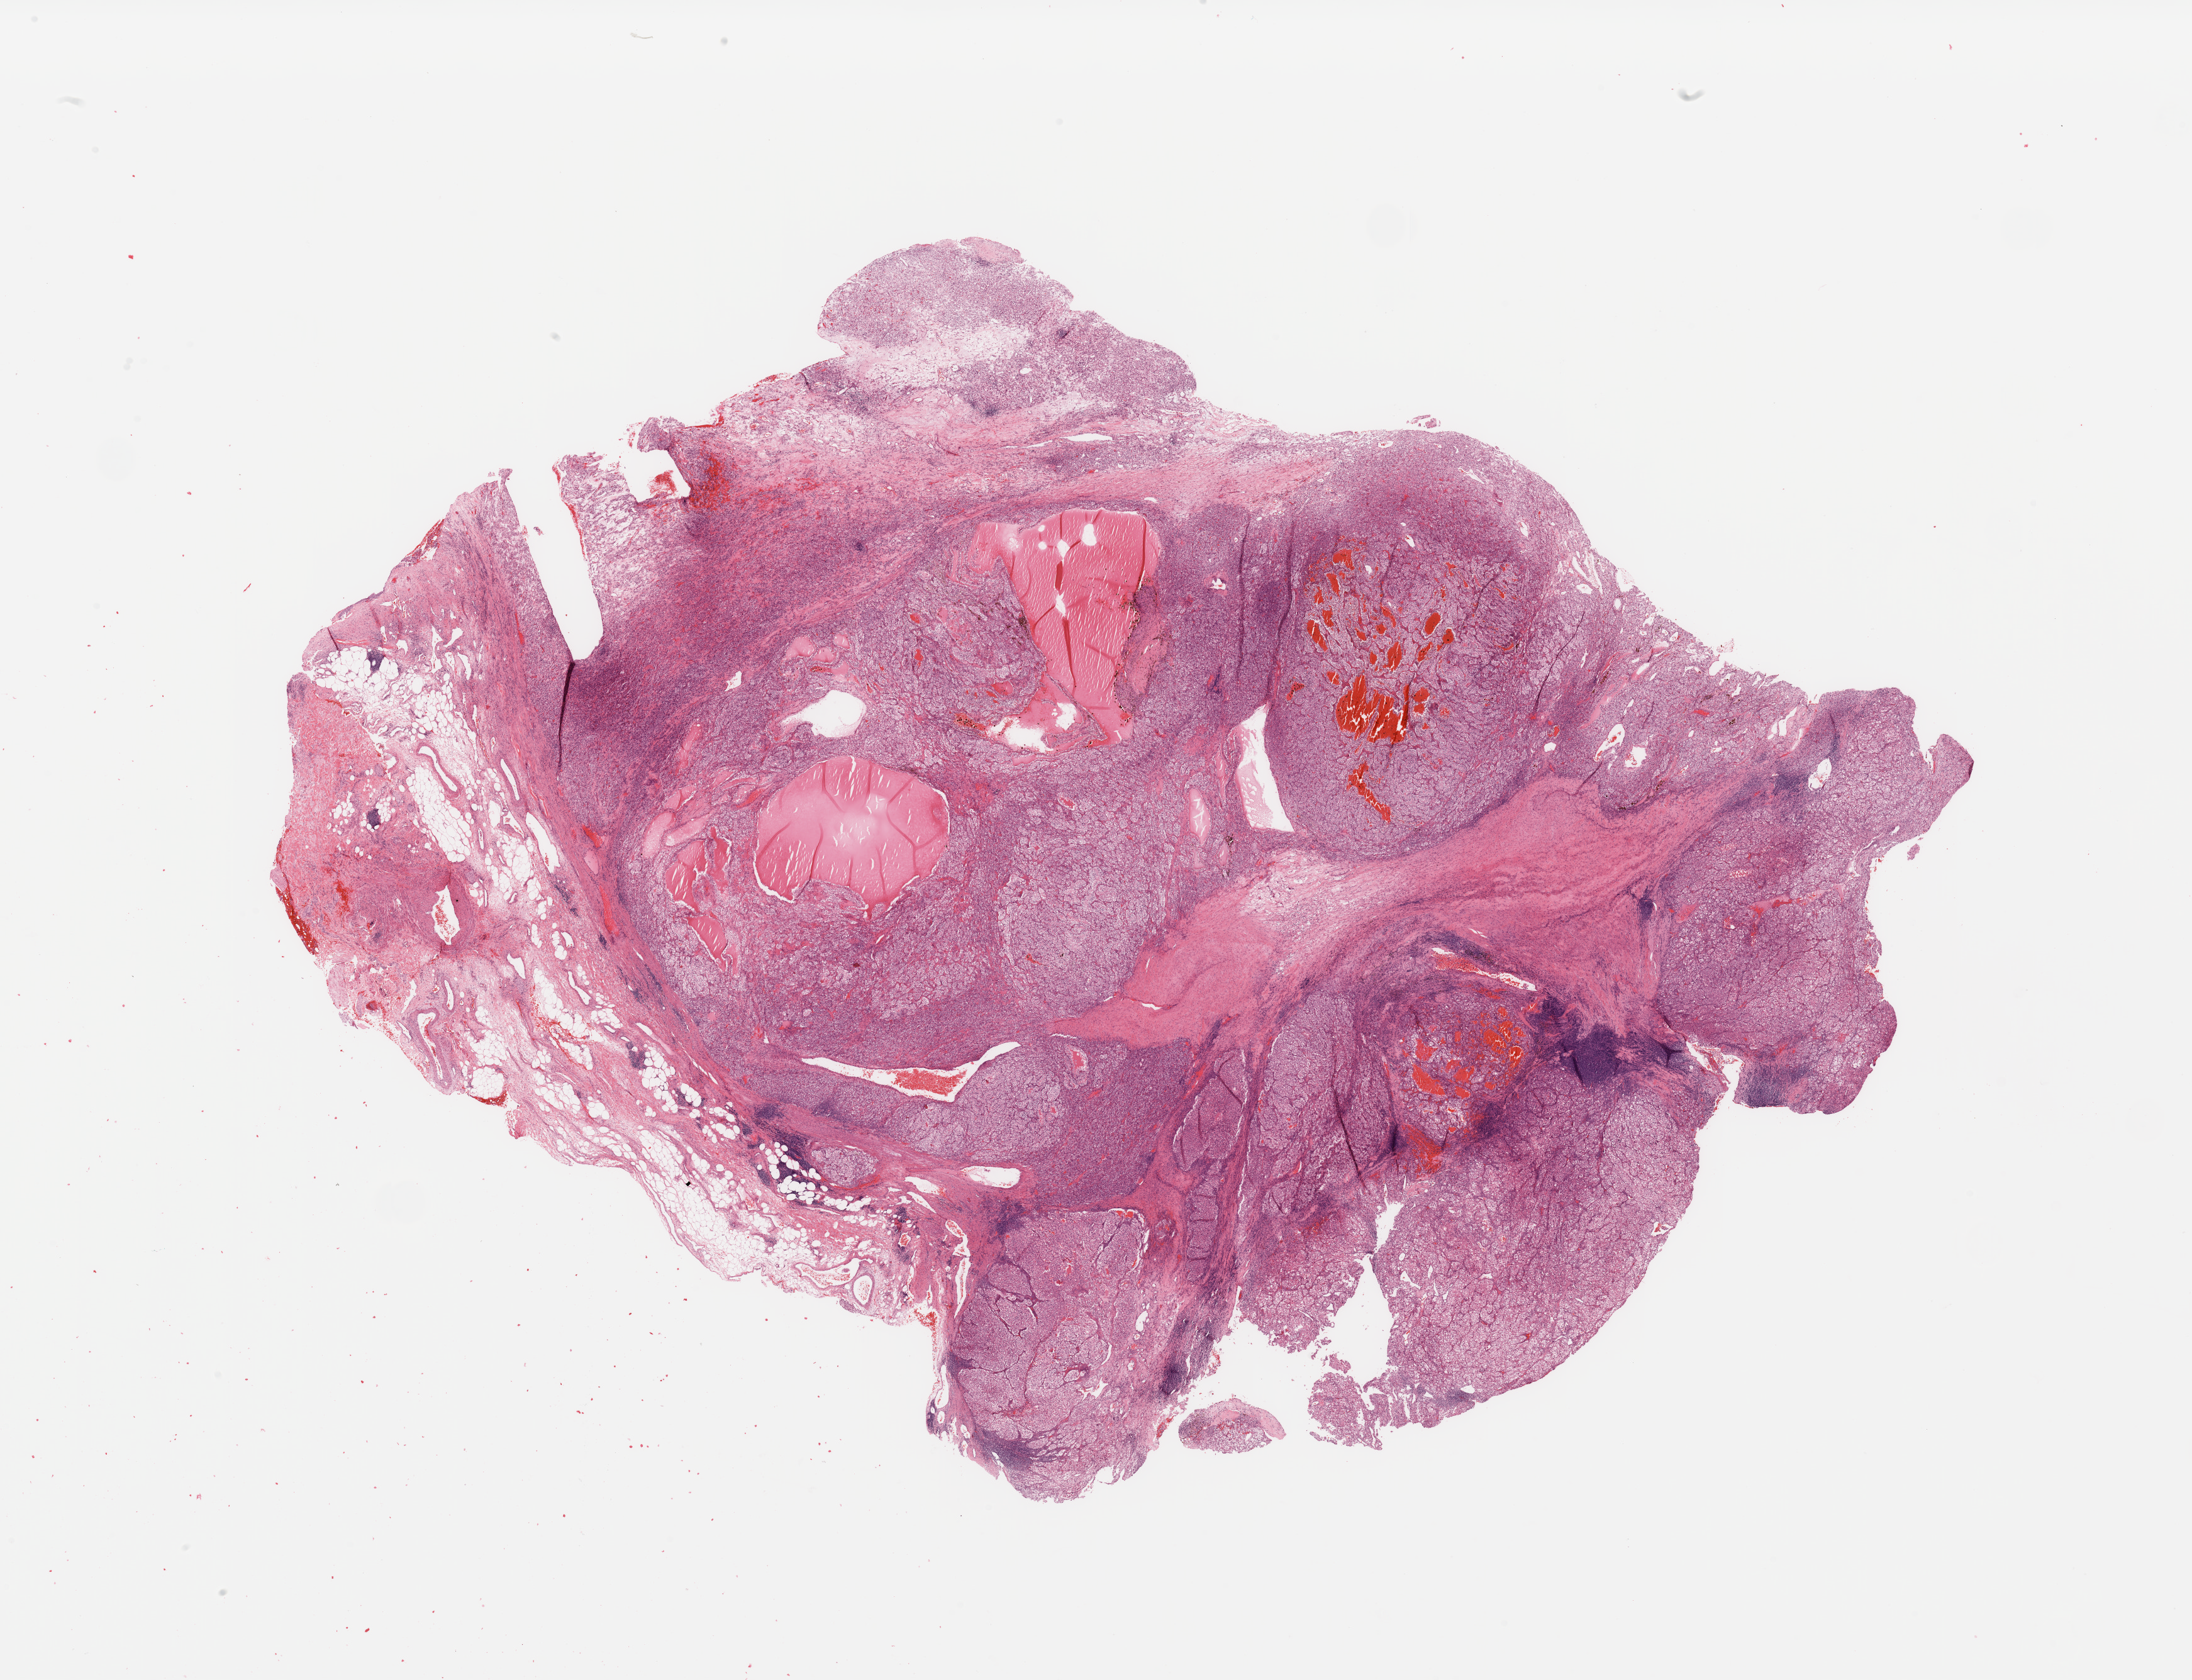
Whole-slide histology image, H&E, whole scanned area (about 27.6 x 21.1 mm, slide scanned at 20x) shown as a low-resolution overview, kidney, tumour tissue. Male, 53 y/o. Histologic grade: G3 (poorly differentiated).
Histologic diagnosis: Renal cell carcinoma, NOS.